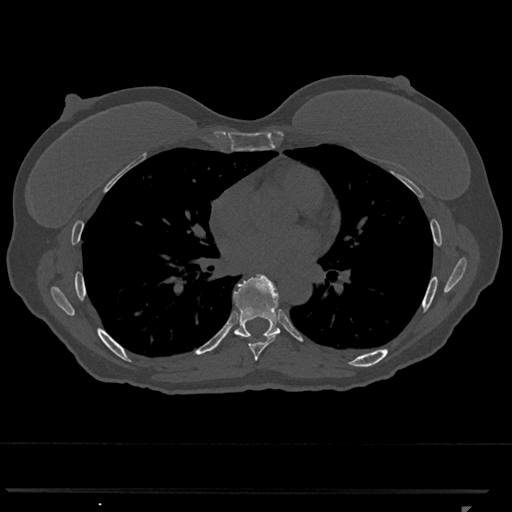
CT including the spine, one axial slice; position 689 of 793 along the scan axis; reconstruction kernel Br40s/3; bone window (W 1800 / L 400 HU); 0.5 mm slice thickness; 512 × 512 image matrix, field of view 380 × 380 mm. Patient: female, 62 years. From the clinical record (not read from this slice): primary cancer: renal.
Structures marked on this image (semi-automatically segmented with operator editing):
- T7 vertebra: box from (x=239, y=334) to (x=278, y=361) px
- T8 vertebra: (x=234, y=274)–(x=281, y=337)